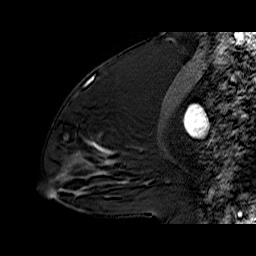
Breast MRI (dynamic contrast-enhanced), one sagittal slice. Position 28 of 60 along the scan axis. Dynamic contrast-enhanced series, time point 2 of 6 at this slice position (early post-contrast). 1.5 T. TE 6.3 ms, TR 32.9 ms. 4 mm slice thickness. 256 × 256 image matrix, field of view 200 × 200 mm. Female patient. Case-level facts recorded for this patient, not image findings: setting: breast cancer imaged before/during neoadjuvant chemotherapy; receptor status: triple-negative.
Structures marked on this image (semi-automatic segmentation, software-assisted and operator-edited):
- analysis volume of interest (the breast-tissue region the enhancement analysis was run in; not a lesion): bounding box <64,79,122,170> (left, top, right, bottom; pixels)
- tumour enhancement mask (voxels above the 100 % enhancement threshold inside the analysis volume of interest): <91,142,108,163>